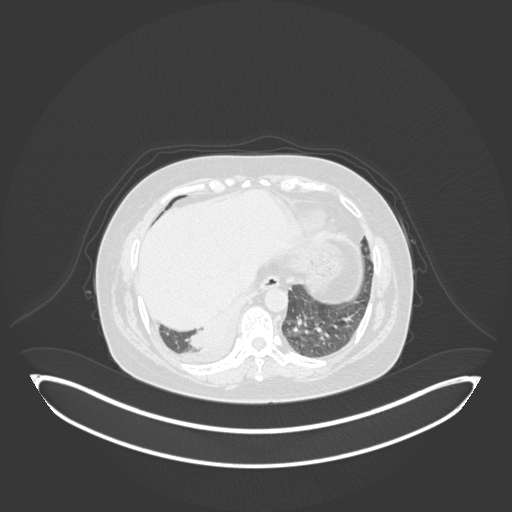
Chest CT, one axial slice; slice 28 of 231 in the series (ordered by position); 120 kVp; lung window (W 1500 / L -600 HU); 1 mm slice thickness; 512 × 512 image matrix. Female patient, age 56 years. Case-level facts recorded for this patient, not image findings: clinical TNM (as recorded): T2b N1 M0.
Outlined on this slice (bounding box drawn by a radiologist):
- lung tumour (recorded histology: small cell carcinoma): bounding box (x1, y1, x2, y2) in pixels: (187, 316, 229, 351)